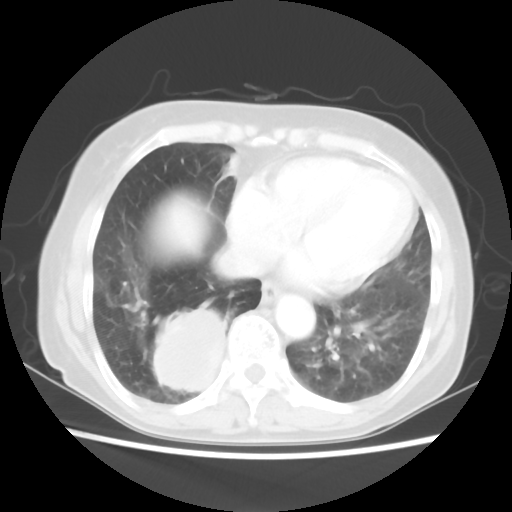
Chest CT, one axial slice; slice 21 of 56 in the series (ordered by position); lung window (W 1500 / L -600 HU); 512 × 512 image matrix, field of view 332 × 332 mm. Patient: female, 66 years. Case-level facts recorded for this patient, not image findings: clinical TNM (as recorded): T2 N3 M0; histopathological grade: G3.
Annotated regions visible in this slice (rectangle marked by the reading radiologist):
- lung tumour (recorded histology: small cell carcinoma): bounding box <151,297,245,399> (left, top, right, bottom; pixels)